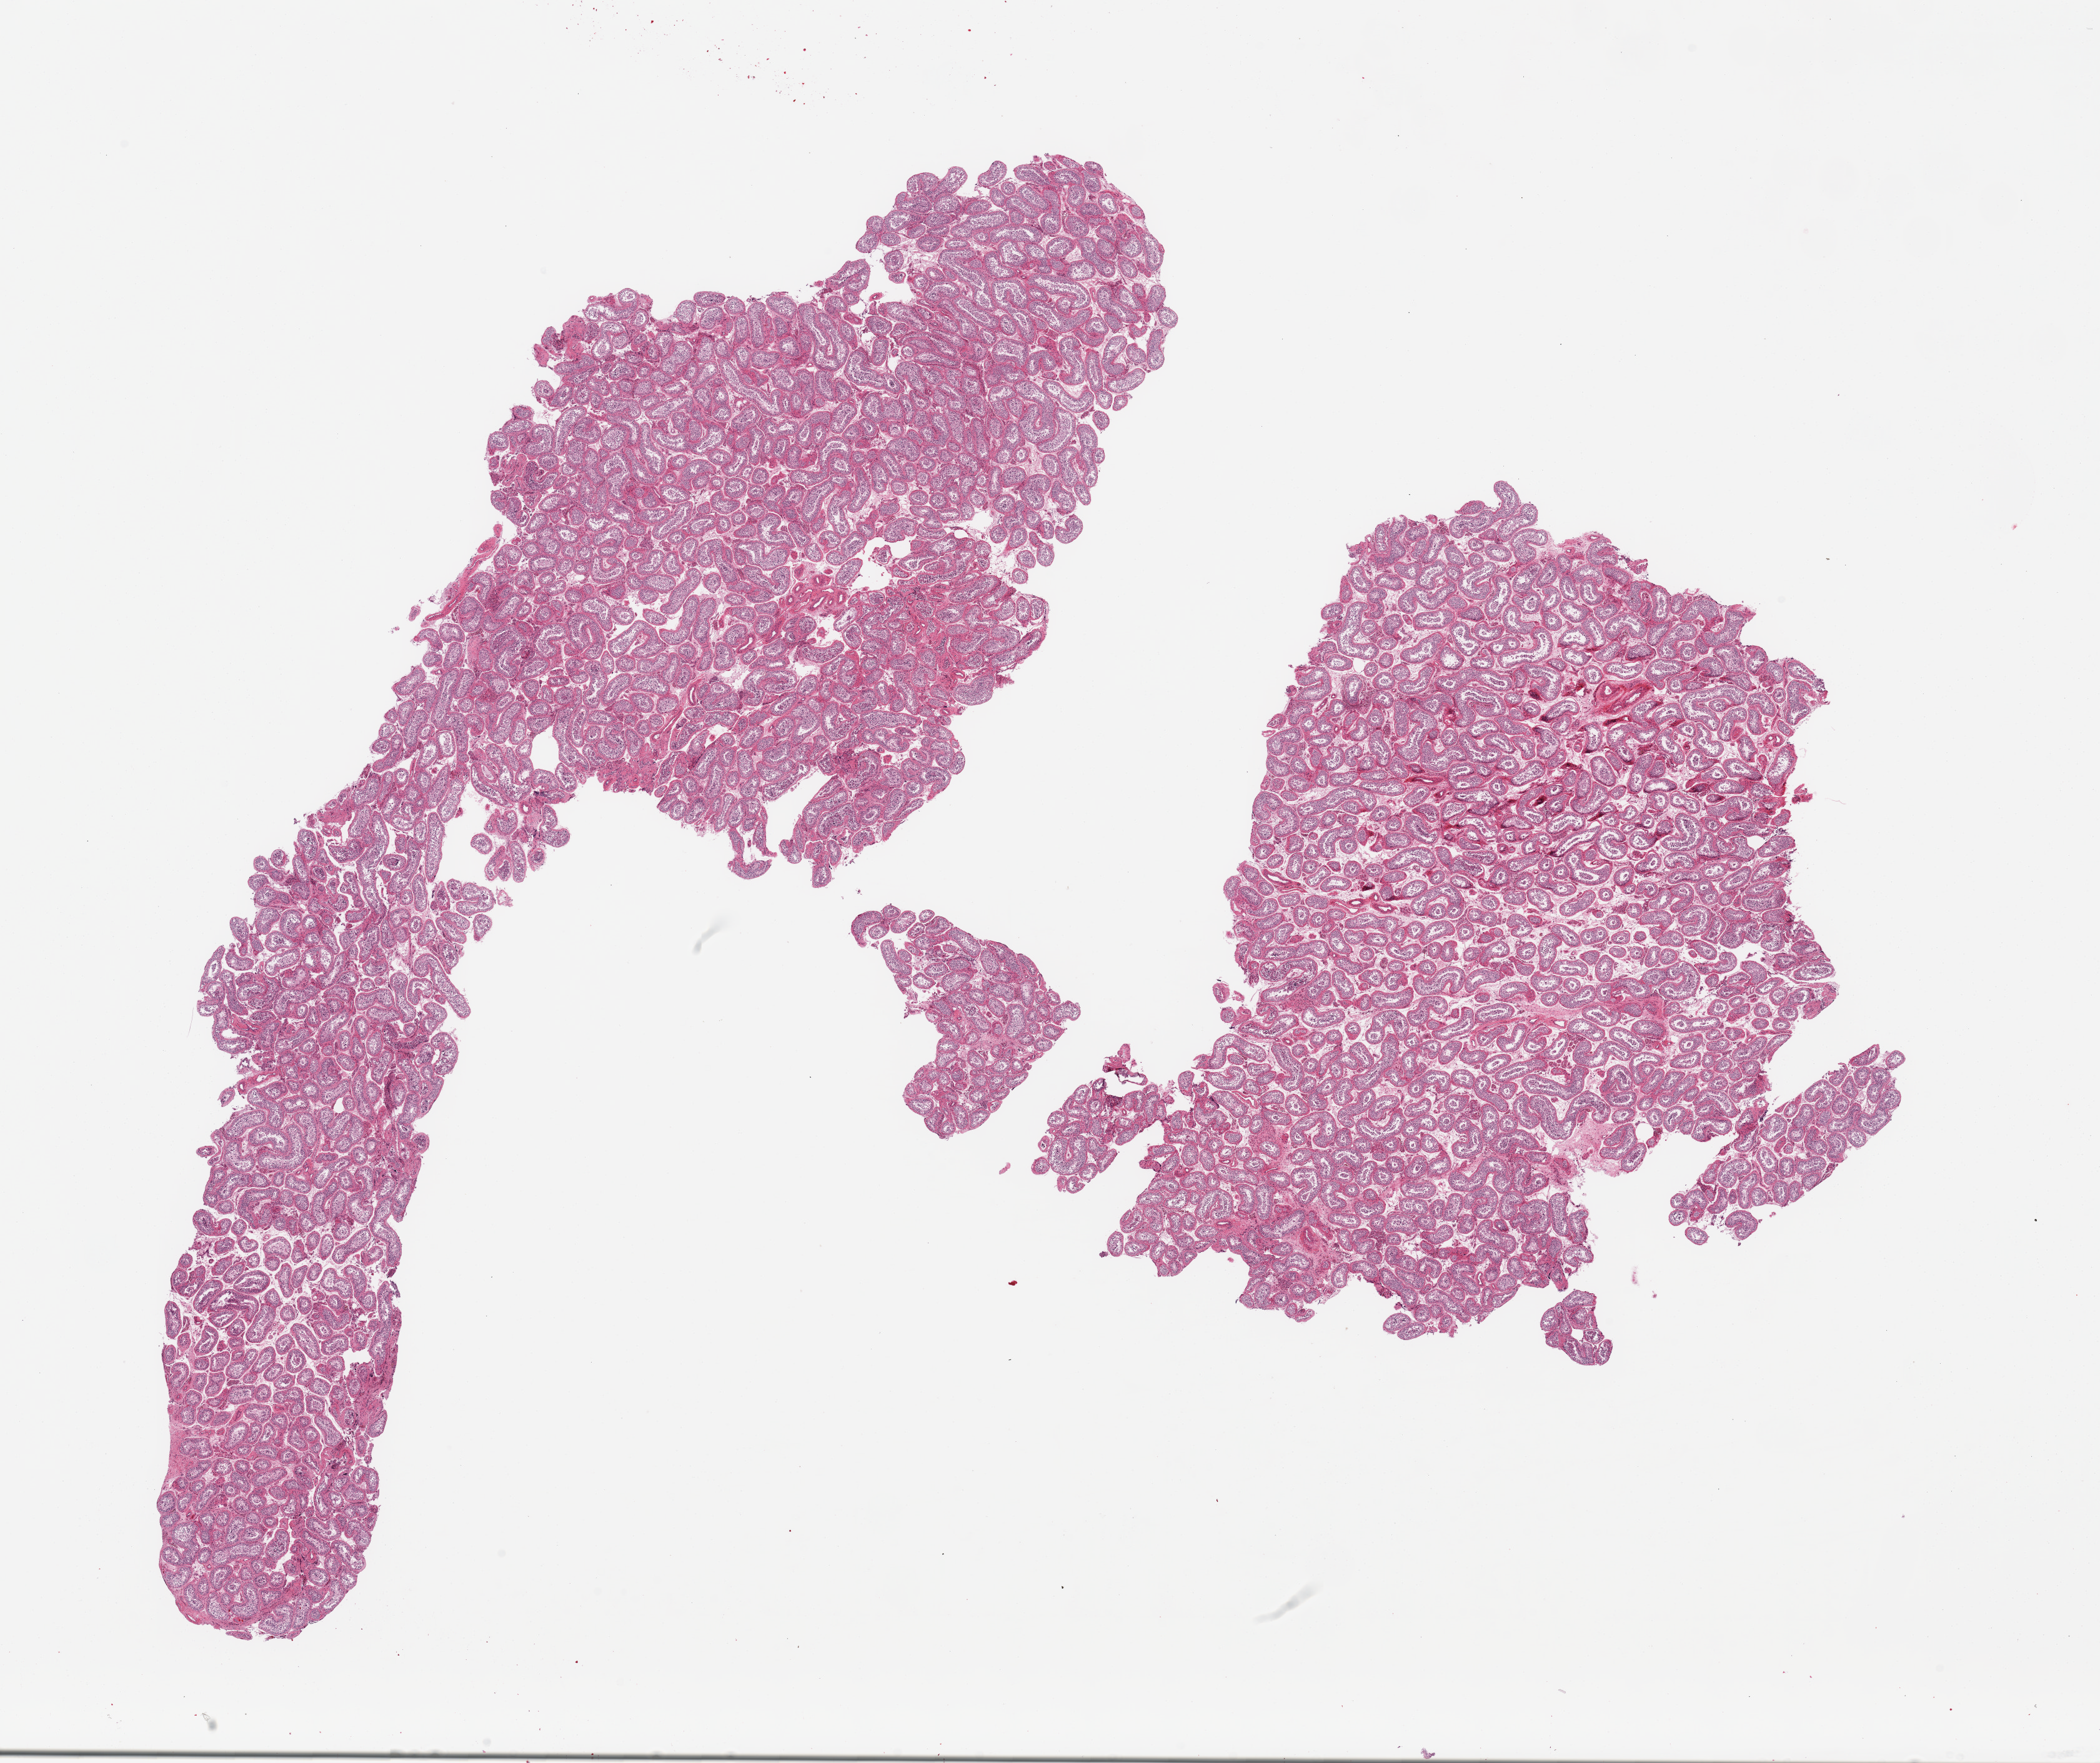
Digitized haematoxylin and eosin-stained section, whole scanned area (about 26.6 x 22.3 mm) shown as a low-resolution overview, PAXgene-fixed paraffin-embedded (PFPE) section, sampled site (target tissue): testis, tissue donor sample. Donor: male.
• reviewer comment on this tissue sample: 2 pieces, spermatogenesis is present but appears reduced